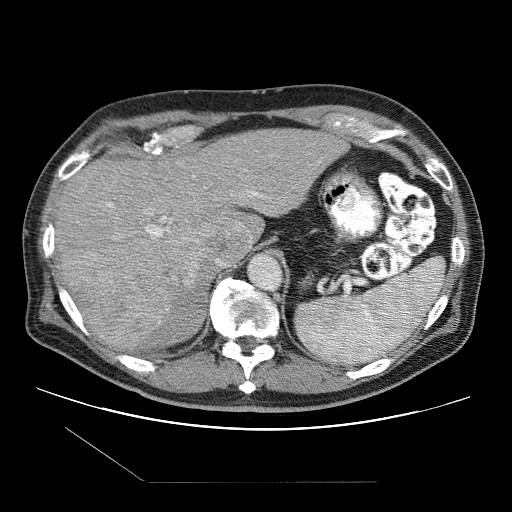
Contrast-enhanced abdominal CT (liver protocol), one axial slice; slice 72 of 109 in the series (ordered by position); reconstruction kernel STANDARD; 120 kVp; one of 2 acquisitions stored at this slice position; soft-tissue window (W 400 / L 40 HU); 512 × 512 image matrix. Case-level facts recorded for this patient, not image findings: diagnosis: hepatocellular carcinoma (patient treated with transarterial chemoembolisation; whether this scan precedes or follows treatment is not stated here); TNM stage (as recorded): Stage-IIIB; Child-Pugh class: A; tumour differentiation: well differentiated; tumour nodularity: multinodular.
Annotated regions visible in this slice (semi-automatic segmentation, software-assisted and operator-edited):
- liver parenchyma outside the tumour (the mass and vessels are separate outlines, so this box may not span the whole liver): bounding box (x1, y1, x2, y2) in pixels: (54, 128, 348, 348)
- mass: (61, 245, 211, 351)
- liver vessels: (108, 191, 262, 237)